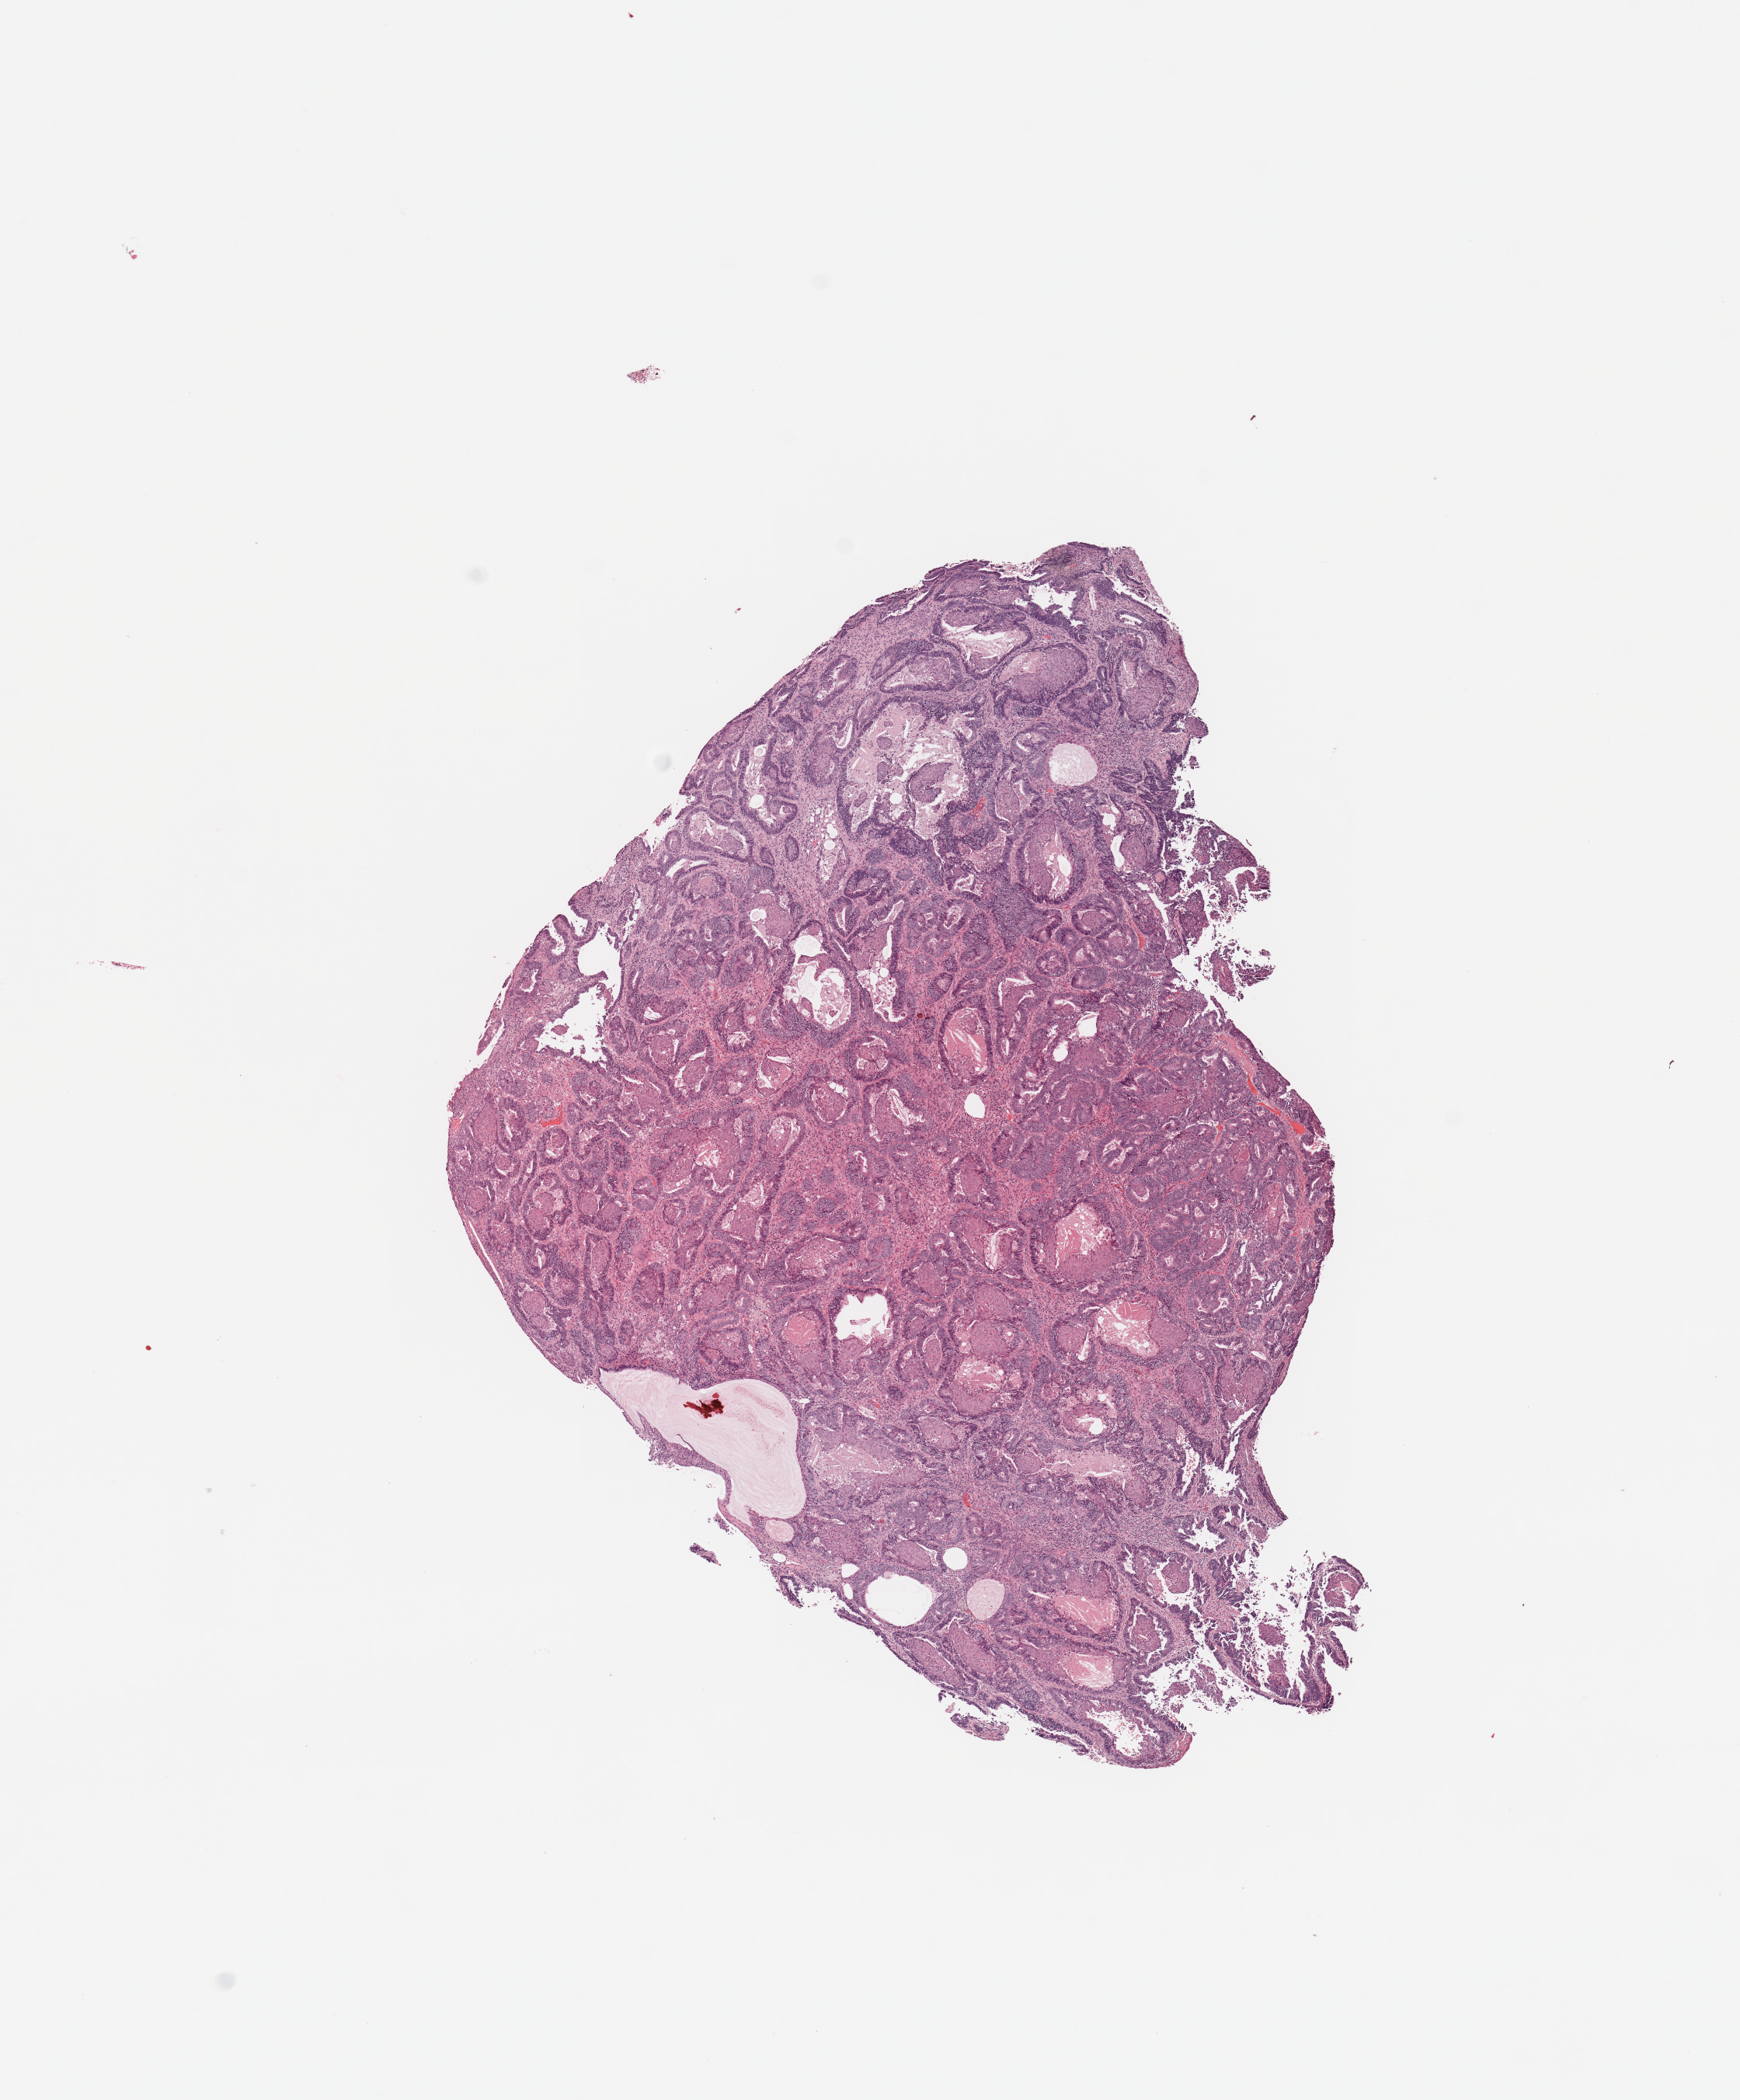
Digitized H&E-stained tissue section (whole slide) — low-resolution overview of the scanned area, about 8.9 x 10.7 mm (acquisition: 20x scan); tumour tissue sample, sampled site: uterus. Patient: female, age 71 years.
Histologic diagnosis: Endometrioid adenocarcinoma, NOS.